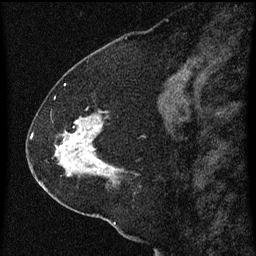
Breast MRI (dynamic contrast-enhanced), one sagittal slice. Position 26 of 60 along the scan axis. Dynamic contrast-enhanced series, image 2 of 3 at this slice position (ordered by acquisition). 1.5 T. TE 4.2 ms, TR 8 ms. 2 mm slice thickness. 256 × 256 image matrix. Patient: female, 47 years.
Annotated regions visible in this slice (semi-automatic segmentation, software-assisted and operator-edited):
- analysis volume of interest (the breast-tissue region the enhancement analysis was run in; not a lesion): bounding box <36,96,141,213> (left, top, right, bottom; pixels)
- tumour enhancement mask (voxels above the 70 % enhancement threshold inside the analysis volume of interest): <54,118,112,177>